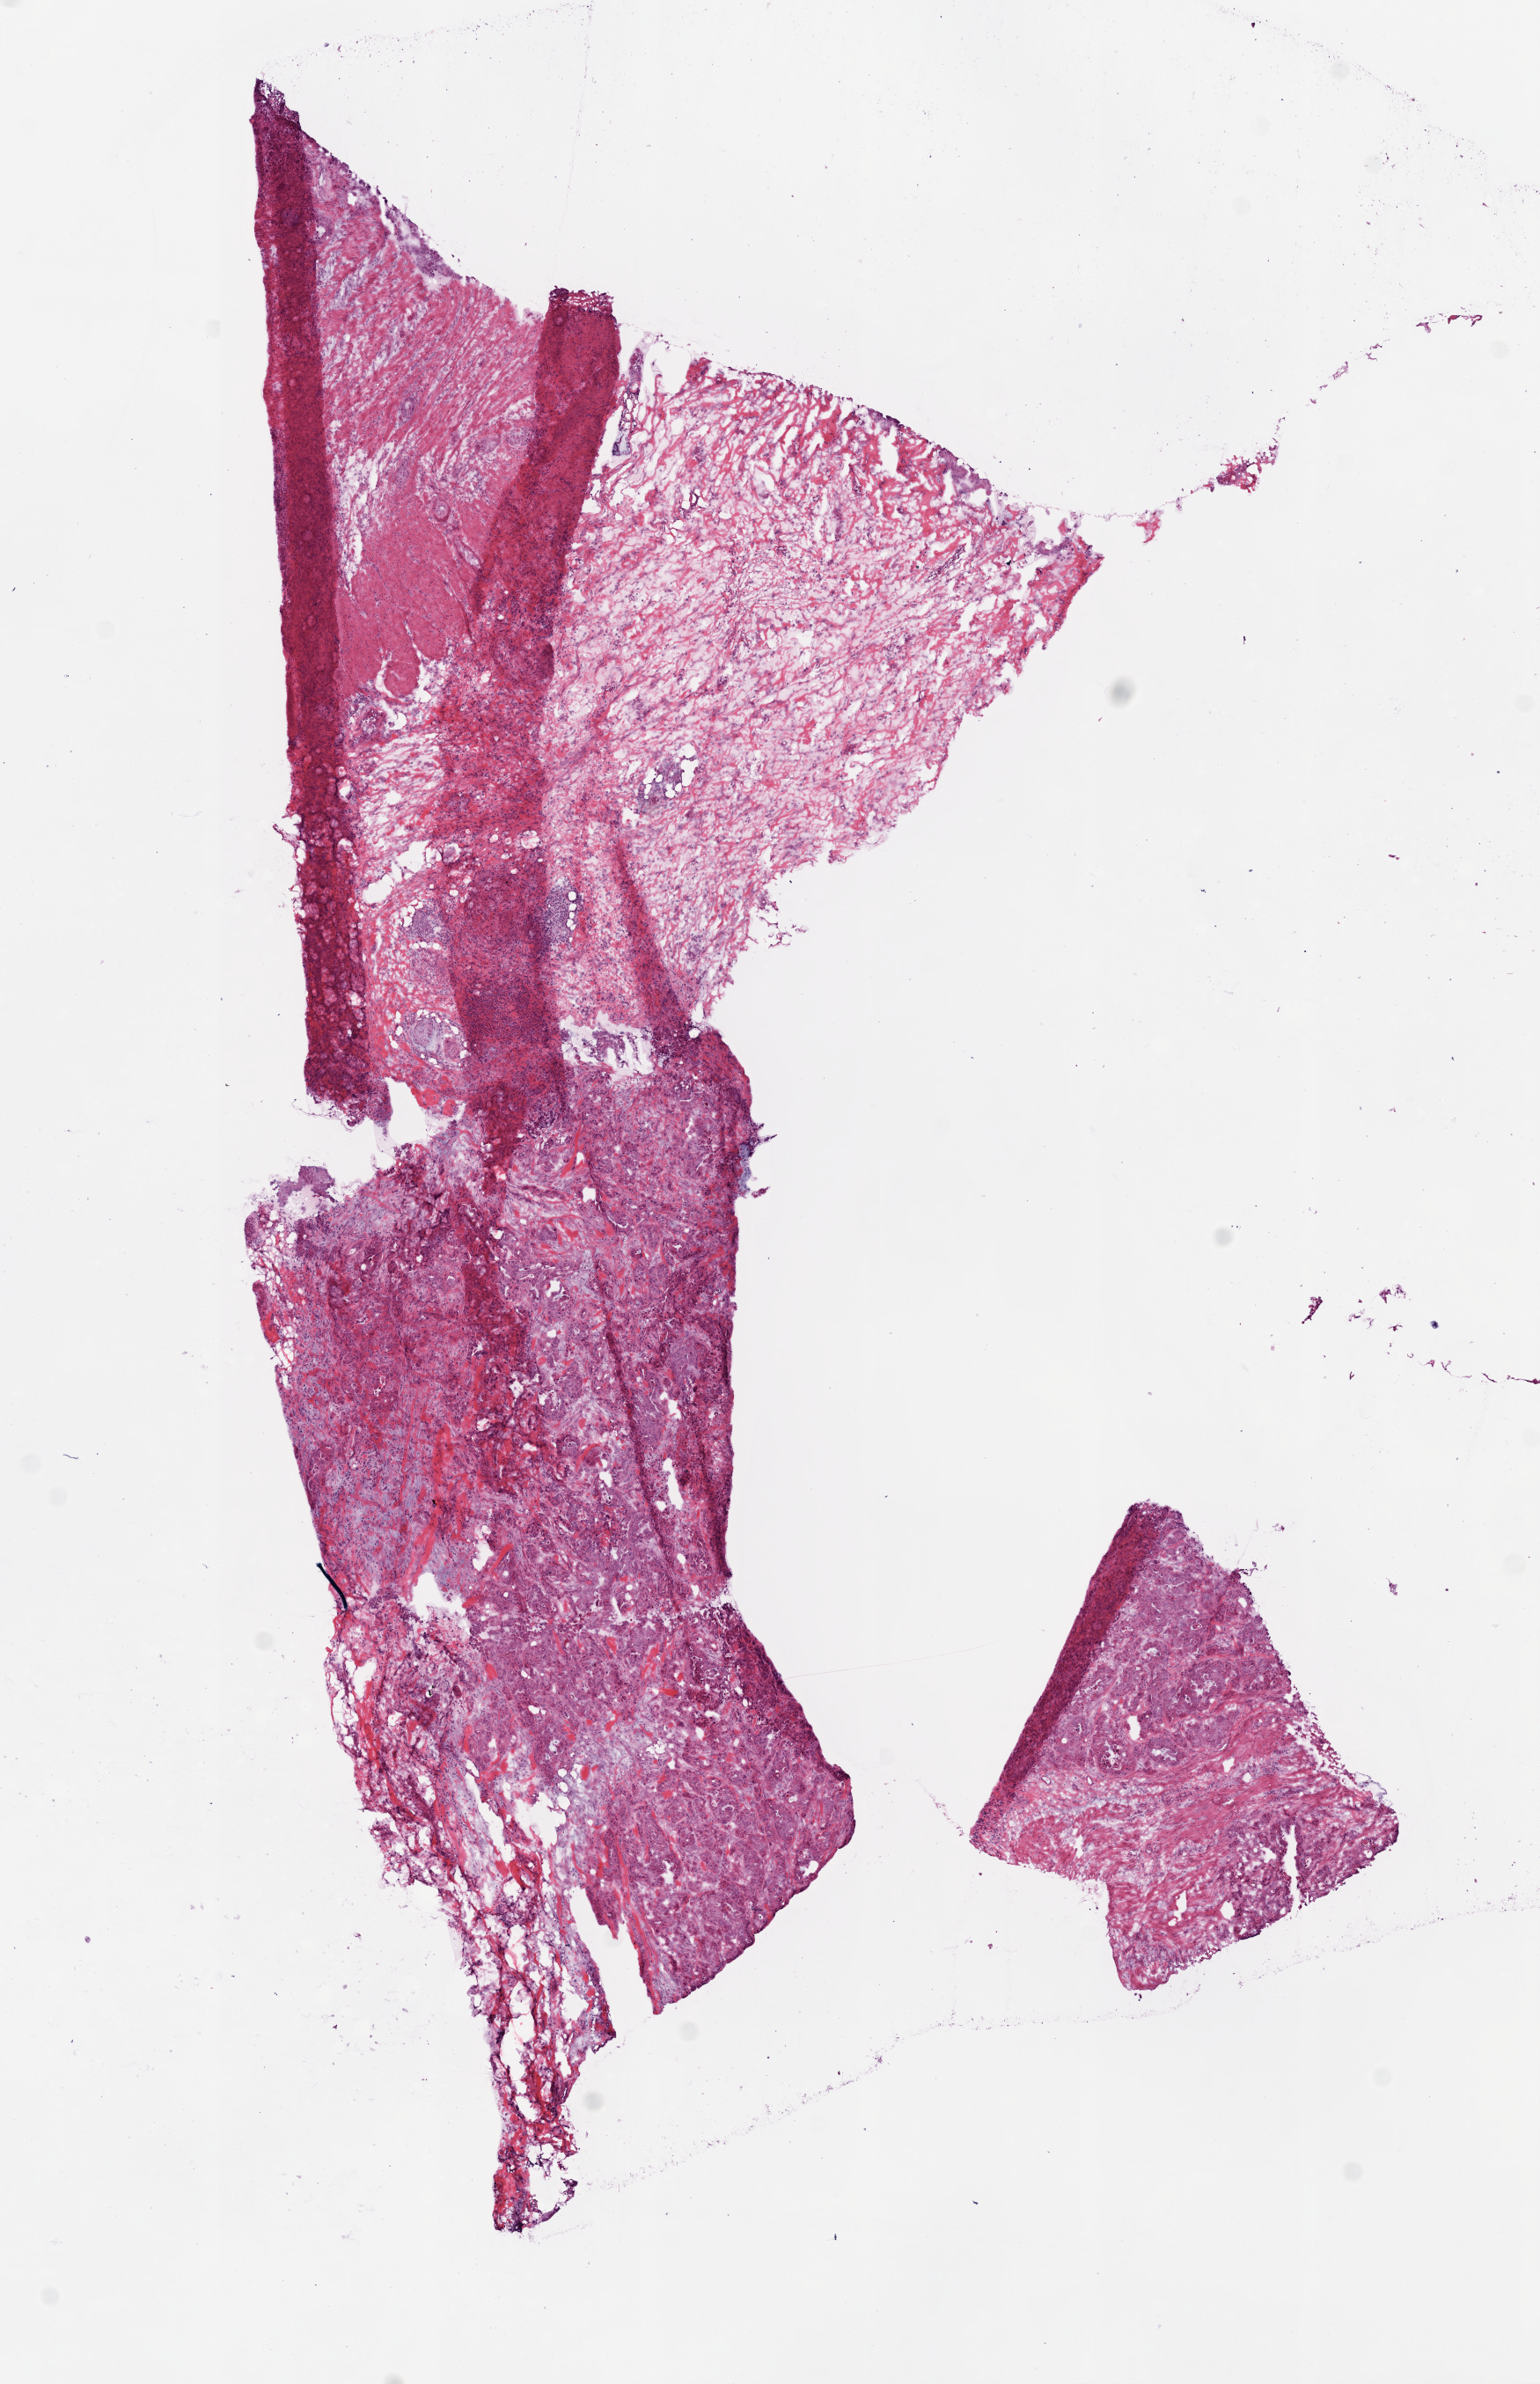
H&E-stained whole-slide image — low-resolution overview of the scanned area, about 7.0 x 10.9 mm, frozen section from the bottom of the tissue portion, sample: primary tumour, colon. Male, age 45 years at initial diagnosis. Composition of this section per pathologist review: tumour cells 52%, tumour nuclei 70%, normal cells 40%, stromal cells 5%, necrosis 3%.
AJCC pathologic stage: IV (6th edition). Lymph nodes positive (case pathology): 23 of 29 examined. Diagnosis: Adenocarcinoma, NOS.